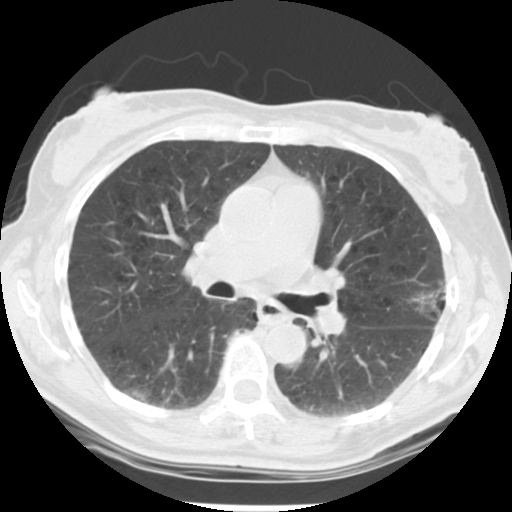
Low-dose screening chest CT, one axial slice; reconstruction kernel STANDARD; 120 kVp; lung window (W 1500 / L -600 HU); 512 × 512 image matrix, field of view 302 × 302 mm.
Structures marked on this image (manually delineated by an expert):
- lesion 1 (tumor, upper lobe of left lung): bounding box [x1, y1, x2, y2] px = [410, 279, 446, 320]